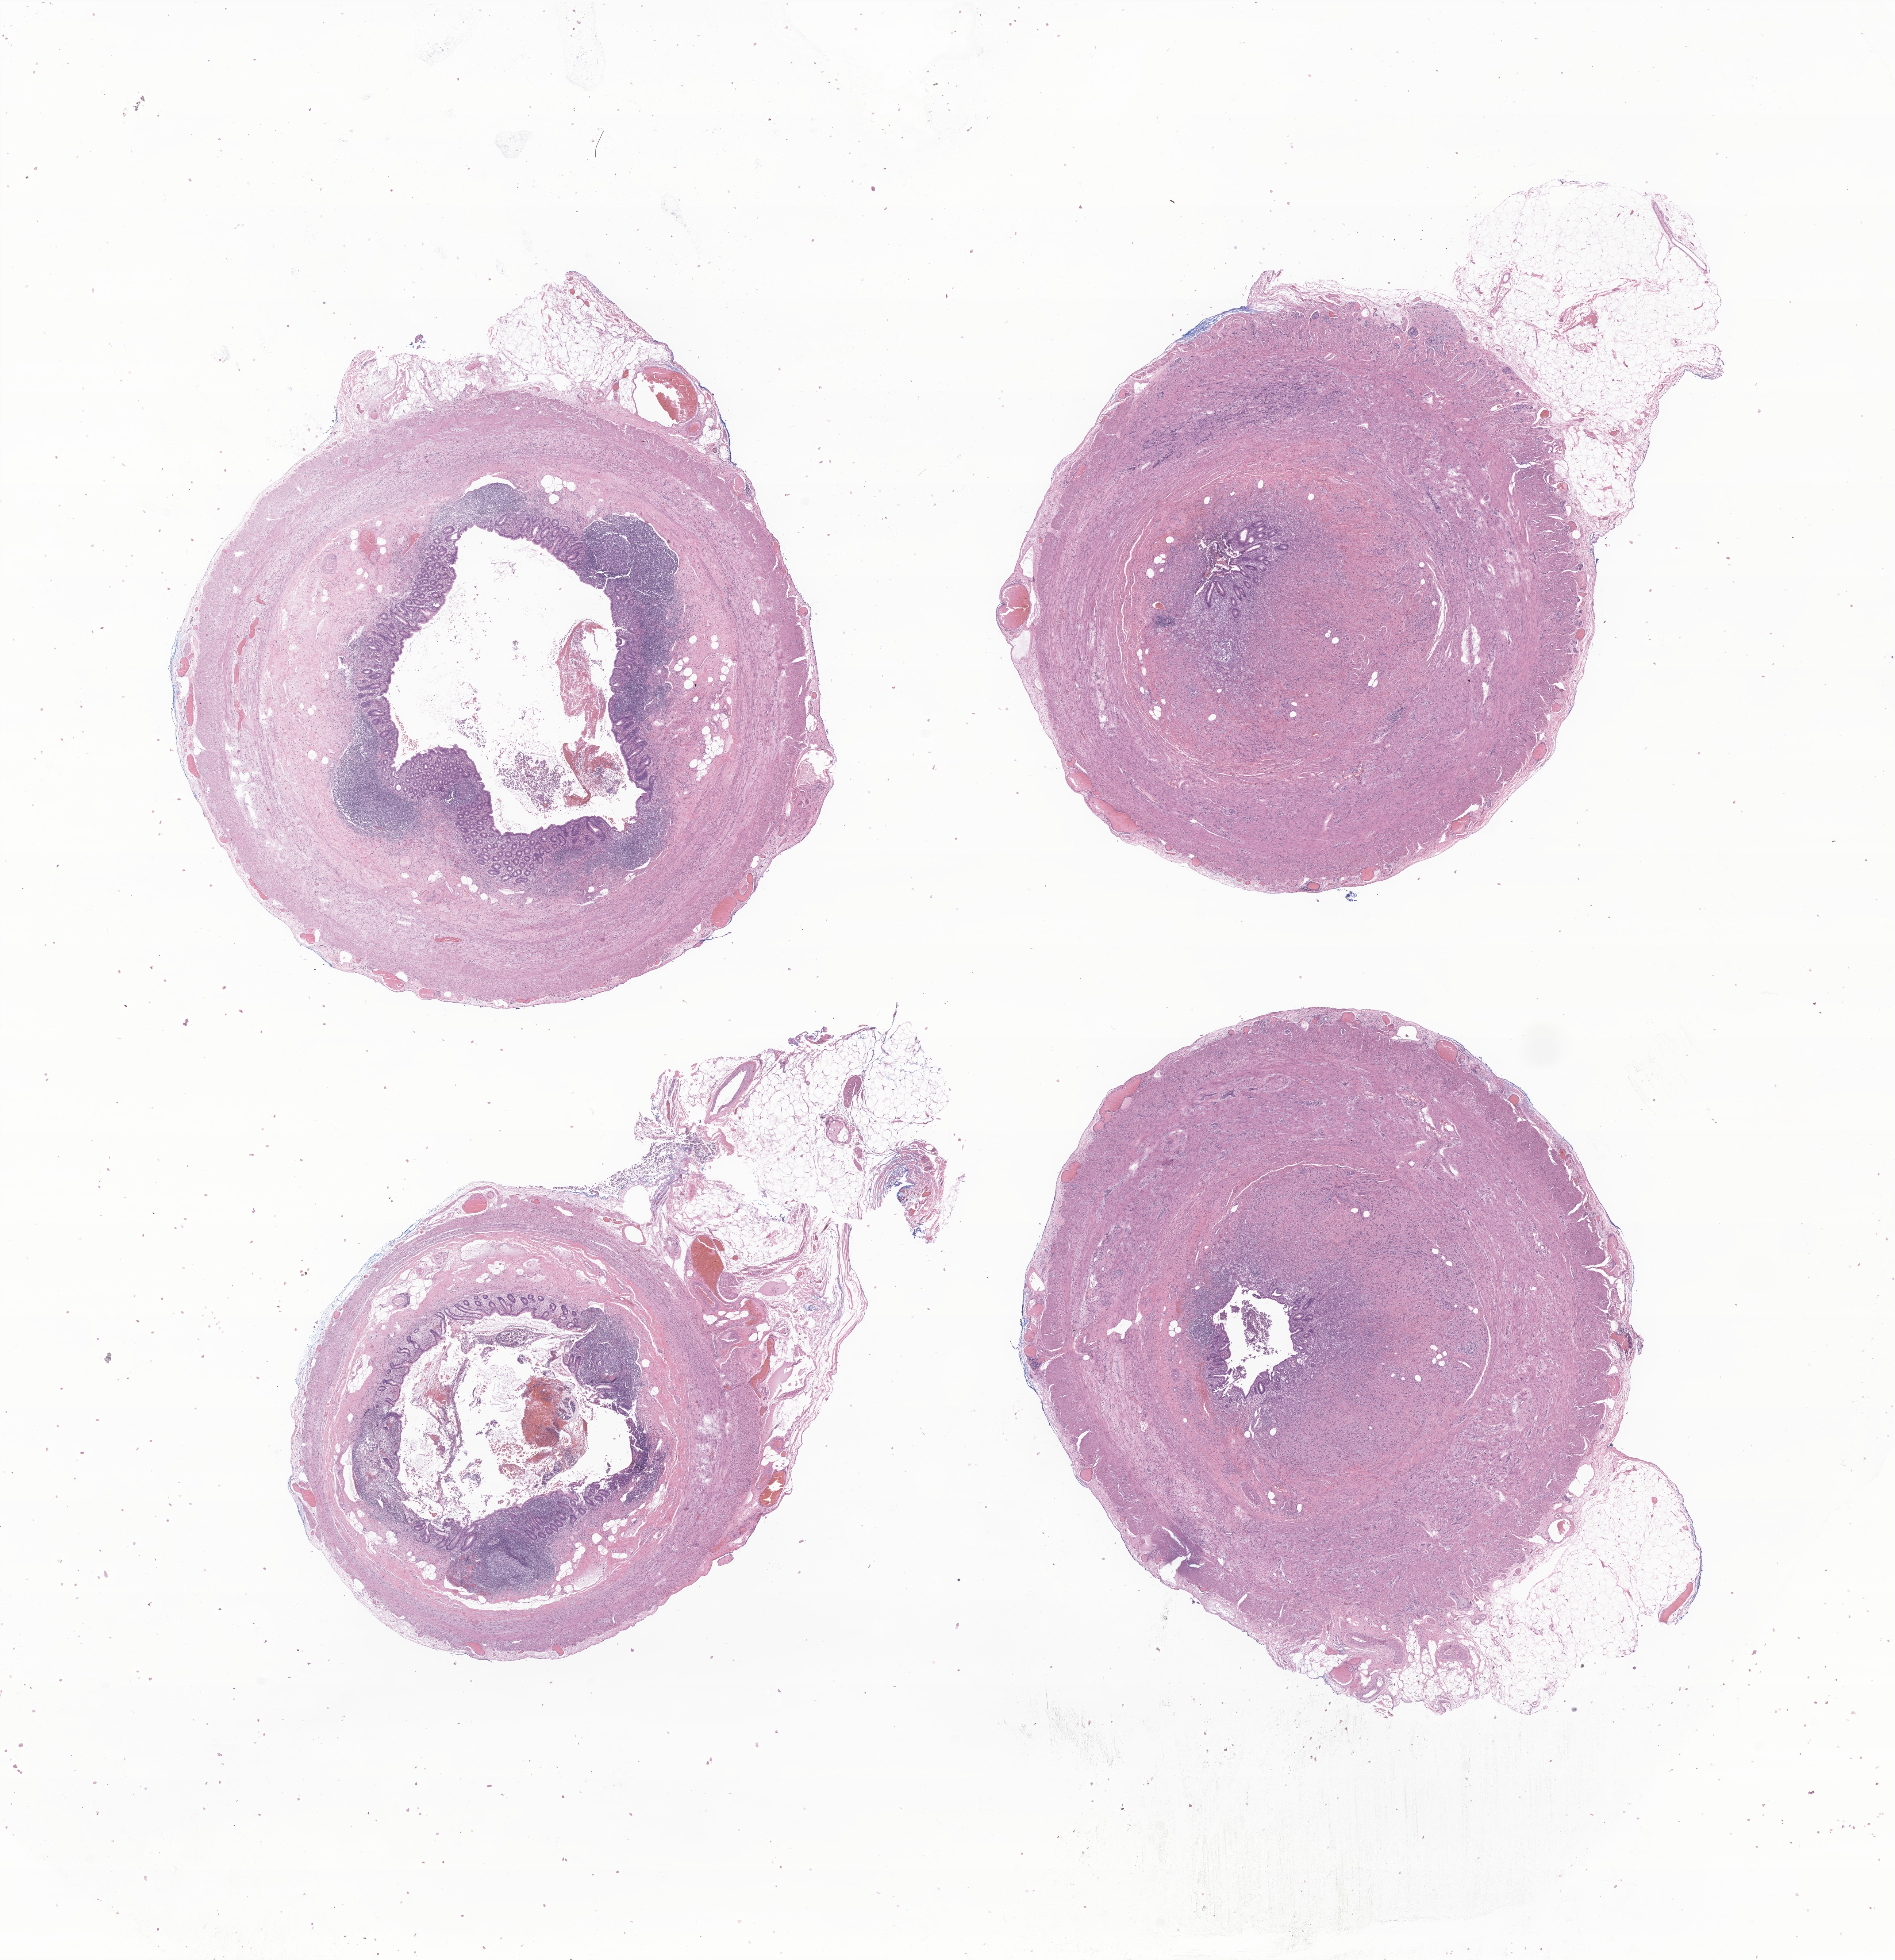
H&E whole-slide image of tumor tissue from the appendix, shown as a low-resolution overview of the whole scanned area (about 21.9 x 22.6 mm), FFPE section. Patient: female, age 200 months (16 years 8 months).
Diagnosis (ICD-O-3 morphology term): Neuroendocrine carcinoma, NOS.